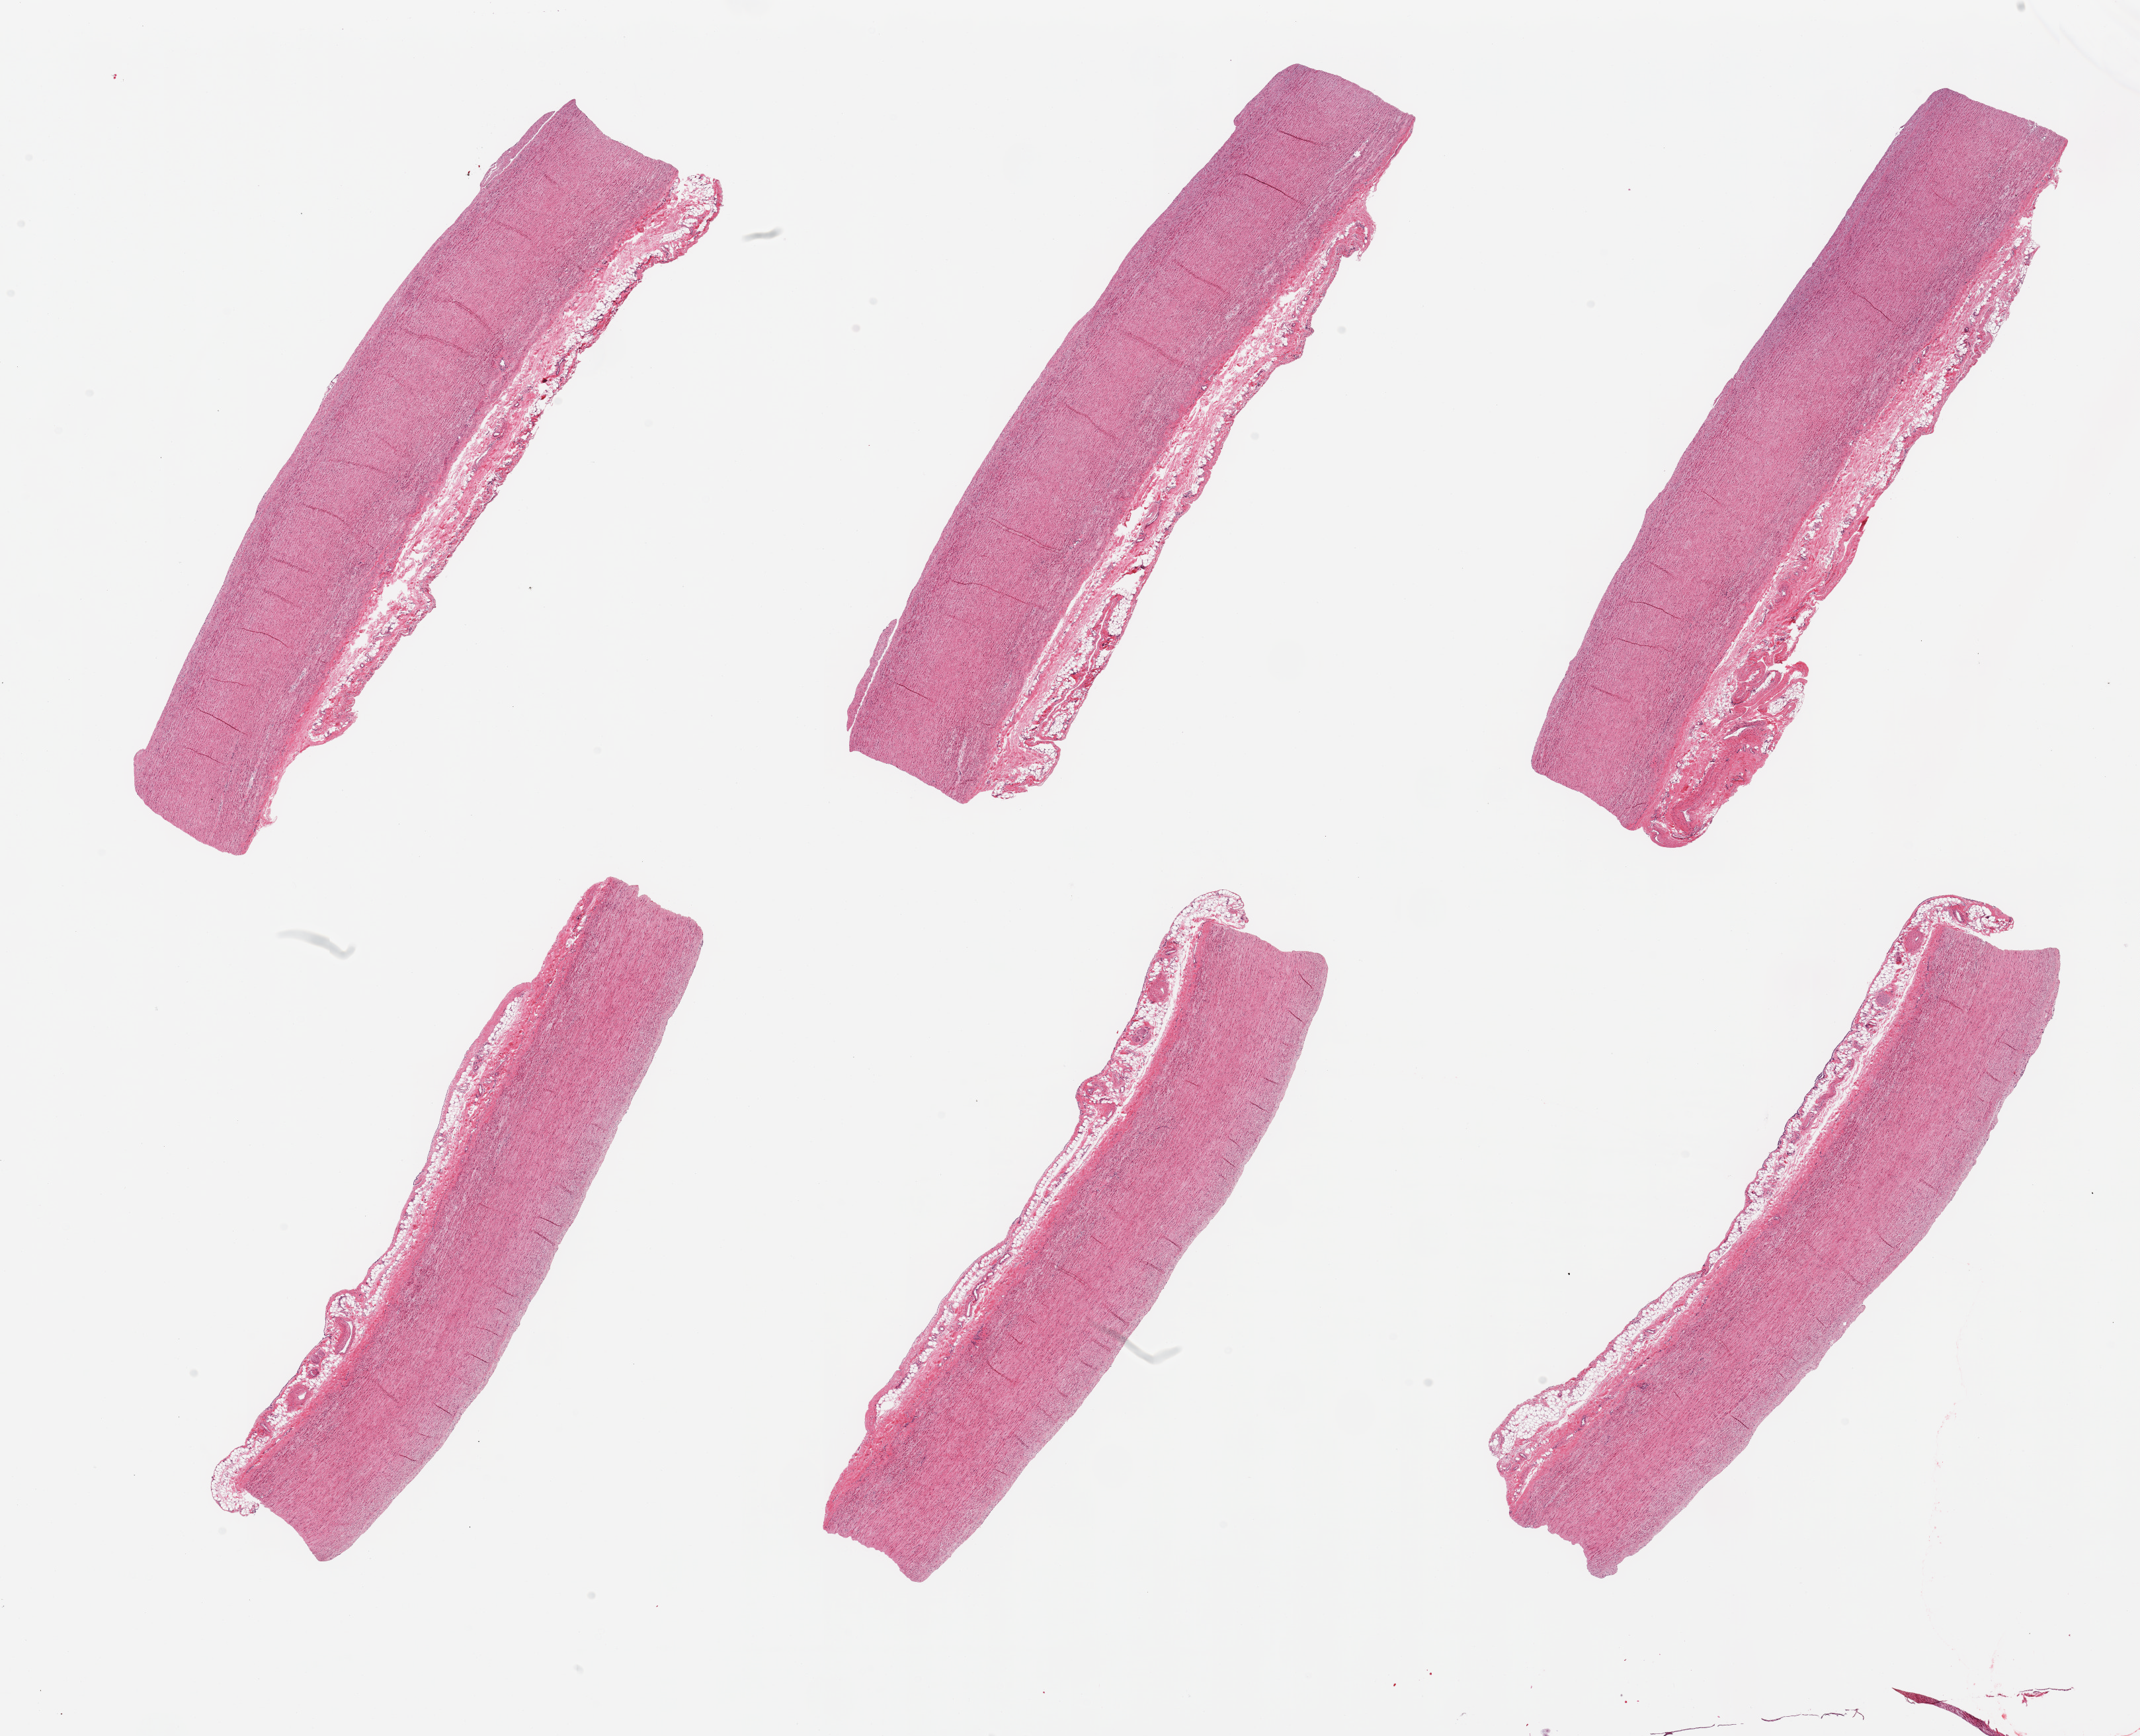
Whole-slide image, H&E stain, brightfield, whole scanned area (about 25.6 x 20.8 mm, acquisition: 20x scan) shown as a low-resolution overview; PAXgene-fixed paraffin-embedded (PFPE) section; sampled site (target tissue): aorta; donor tissue sample. Donor: male.
Pathologist's review note for this sample: 6 pieces, minimal atherosis, adherent fascia/fat up to ~1mm.